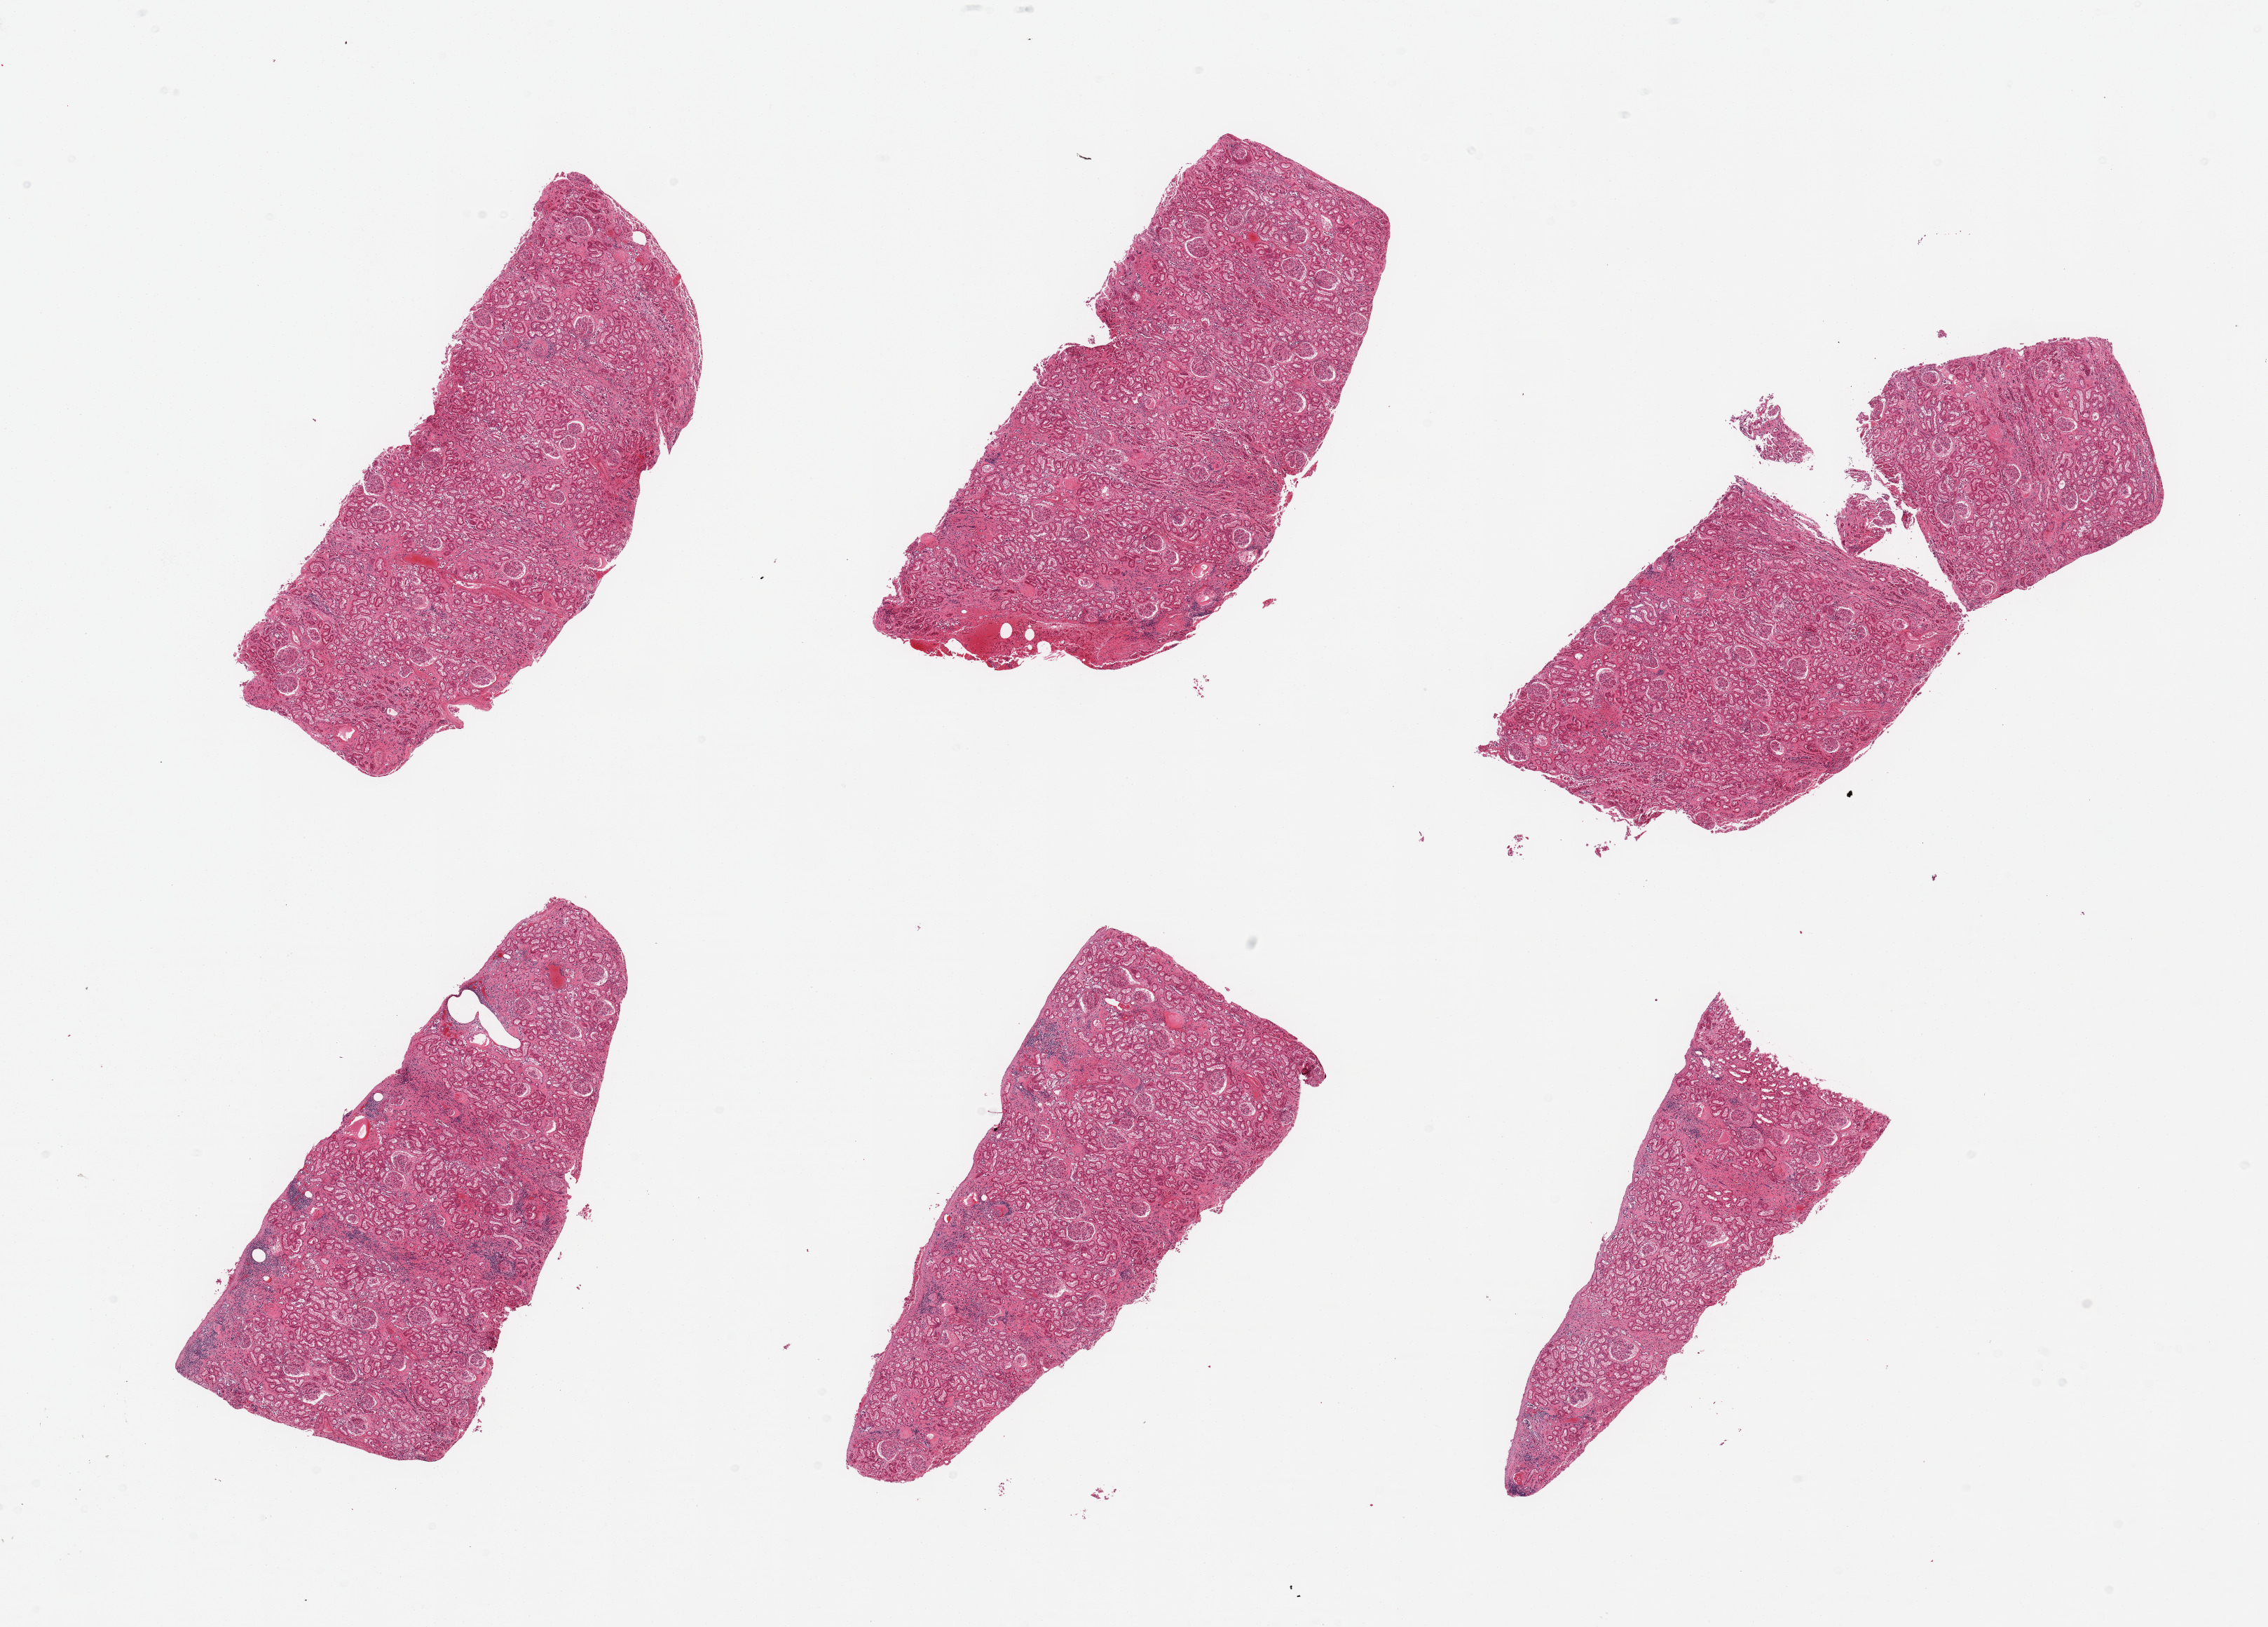
Digitized hematoxylin and eosin (H&E)-stained section, shown as a low-resolution overview of the whole scanned area (about 25.6 x 18.4 mm, from a 20x scan). PAXgene-fixed, paraffin-embedded tissue. Section of renal cortex (target tissue). Donor tissue sample. Donor: male.
Reviewer comment on this tissue sample: 6 pieces, glomeruli present; tubules with advanced autolysis/sloughing.